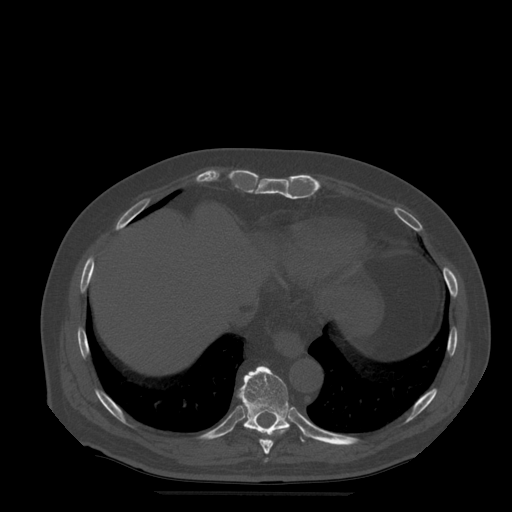
CT including the spine, one axial slice. Slice 277 of 522 in the series (ordered by position). Bone window (W 1800 / L 400 HU). 512 × 512 image matrix. Patient age 72 years. Case-level facts recorded for this patient, not image findings: primary cancer: prostate.
Outlined on this slice (semi-automatically segmented with operator editing):
- T10 vertebra: bounding box (x1, y1, x2, y2) in pixels: (238, 366, 310, 442)
- T8 vertebra: (265, 459, 268, 462)
- T9 vertebra: (245, 427, 290, 455)